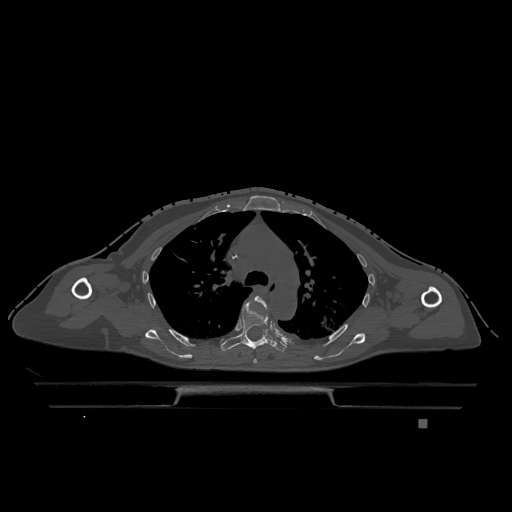
CT including the spine, one axial slice; slice 848 of 1317 in the series (ordered by position); bone window (W 1800 / L 400 HU); 0.5 mm slice thickness; 512 × 512 image matrix, field of view 500 × 500 mm. Patient: female, 74 years. From the clinical record (not read from this slice): primary cancer: lung.
Annotated regions visible in this slice (semi-automatically segmented with operator editing):
- T4 vertebra: bounding box [x1, y1, x2, y2] px = [247, 296, 268, 363]
- T5 vertebra: [221, 302, 287, 353]